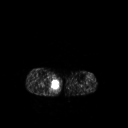
FDG PET of an extremity soft-tissue mass (from a PET/CT study), one axial slice; slice 144 of 267 in the series (ordered by position); 128 × 128 image matrix, field of view 500 × 500 mm. Male patient, age 69 years. Case-level facts recorded for this patient, not image findings: histological type: pleiomorphic liposarcoma; grade: high; site of the primary tumour: right calf.
Structures marked on this image (expert contour drawn on MRI and transferred to this co-registered scan by the dataset authors):
- gross tumour volume including surrounding oedema: bounding box <49,77,60,90> (left, top, right, bottom; pixels)
- gross tumour volume (mass): <52,79,59,88>